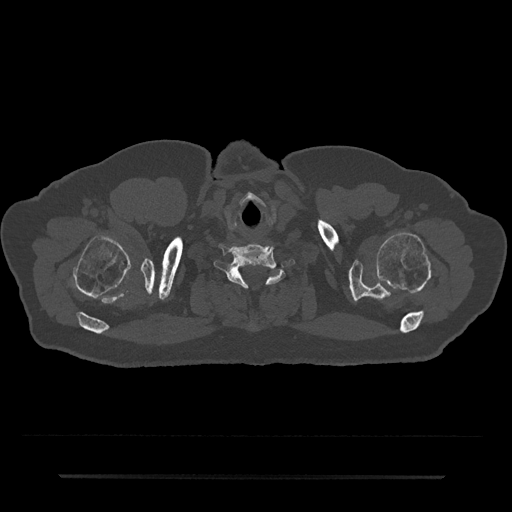
CT including the spine, one axial slice; position 666 of 797 along the scan axis; reconstruction kernel Br40s/3; bone window (W 1800 / L 400 HU); 0.5 mm slice thickness; 512 × 512 image matrix. Patient: male, 69 years. Case-level facts recorded for this patient, not image findings: primary cancer: prostate.
Annotated regions visible in this slice (semi-automatically segmented with operator editing):
- T1 vertebra: bounding box [x1, y1, x2, y2] px = [268, 270, 281, 280]